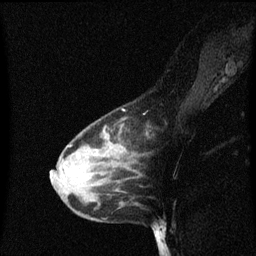
Breast MRI (dynamic contrast-enhanced), one sagittal slice. Position 43 of 60 along the scan axis. Dynamic contrast-enhanced series, image 2 of 3 at this slice position (ordered by acquisition). 1.5 T. TE 4.2 ms, TR 8.4 ms. 2 mm slice thickness. 256 × 256 image matrix, field of view 200 × 200 mm. Patient: female, 38 years. From the clinical record (not read from this slice): setting: breast cancer imaged before/during neoadjuvant chemotherapy; receptor status: HR-positive, HER2-negative.
Annotated regions visible in this slice (semi-automatically segmented with operator editing):
- analysis volume of interest (the breast-tissue region the enhancement analysis was run in; not a lesion): bounding box [x1, y1, x2, y2] px = [50, 118, 139, 205]
- tumour enhancement mask (voxels above the 70 % enhancement threshold inside the analysis volume of interest): [64, 156, 79, 169]